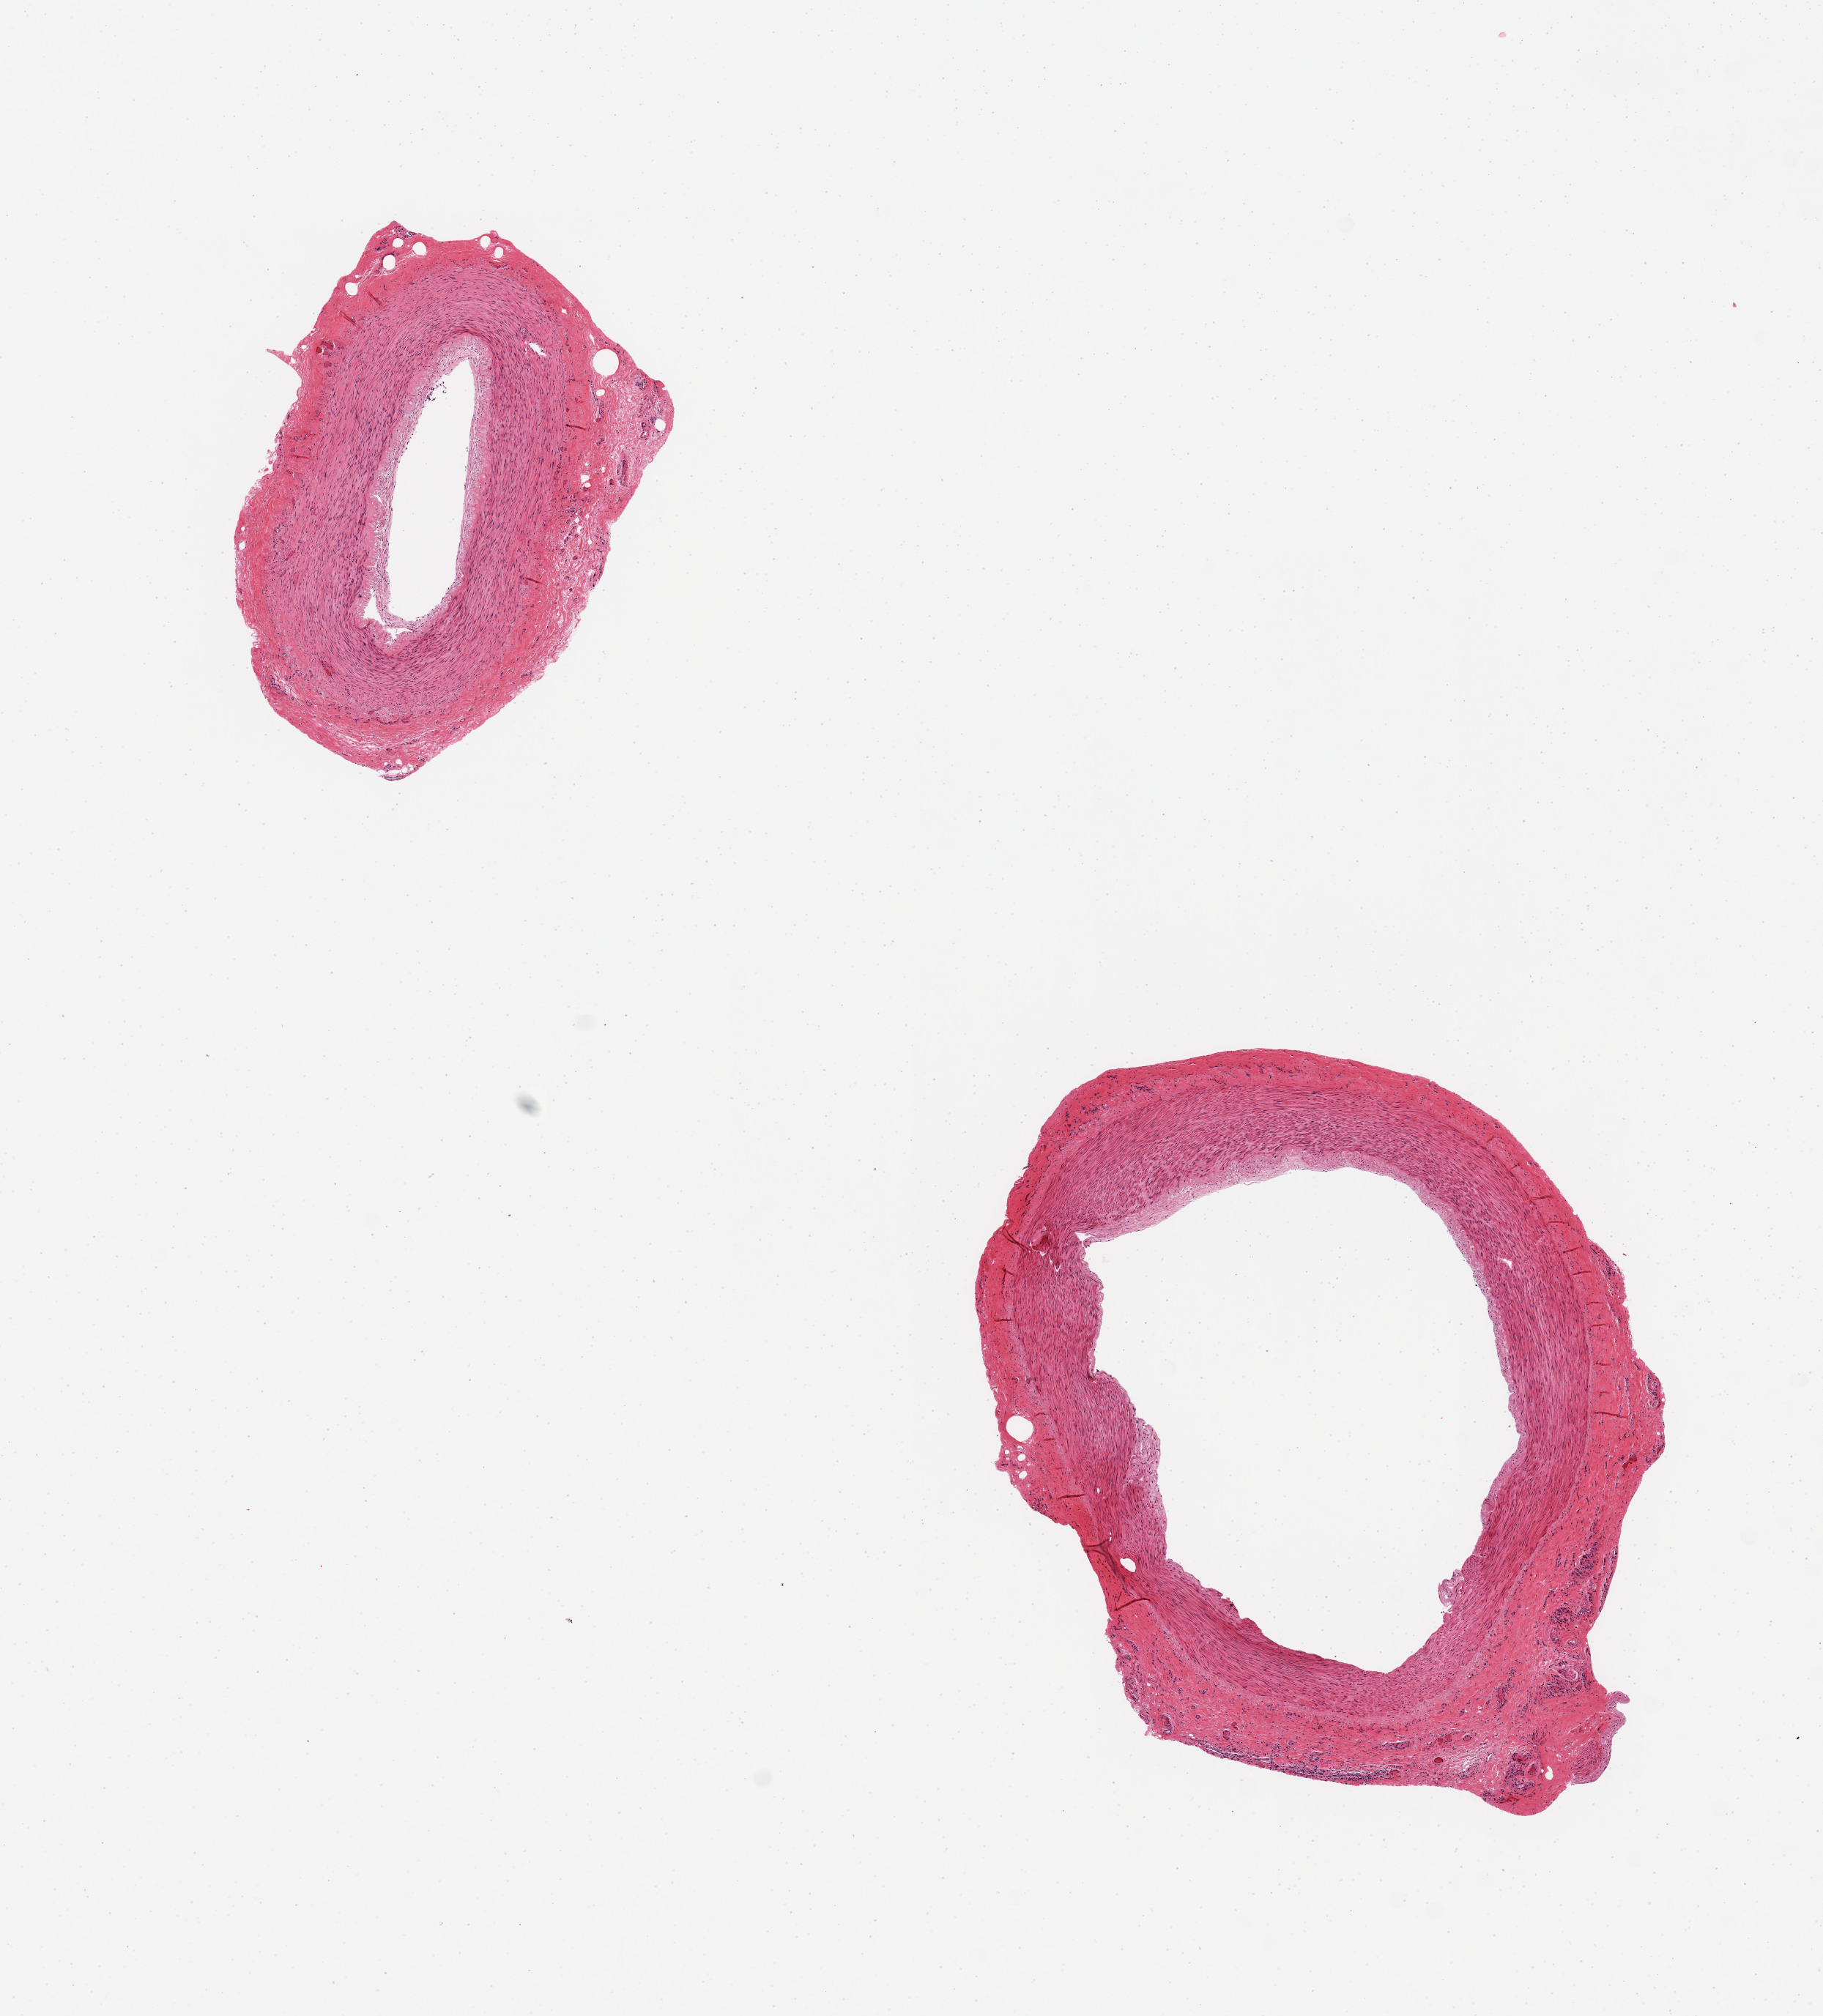
Digitized haematoxylin and eosin-stained section — whole scanned area (about 9.8 x 10.9 mm) shown as a low-resolution overview. PAXgene-fixed, paraffin-embedded tissue. Sampled site (target tissue): tibial artery. Donor tissue sample. Male donor.
• pathologist's review note for this sample: 2 pieces; well trimmed